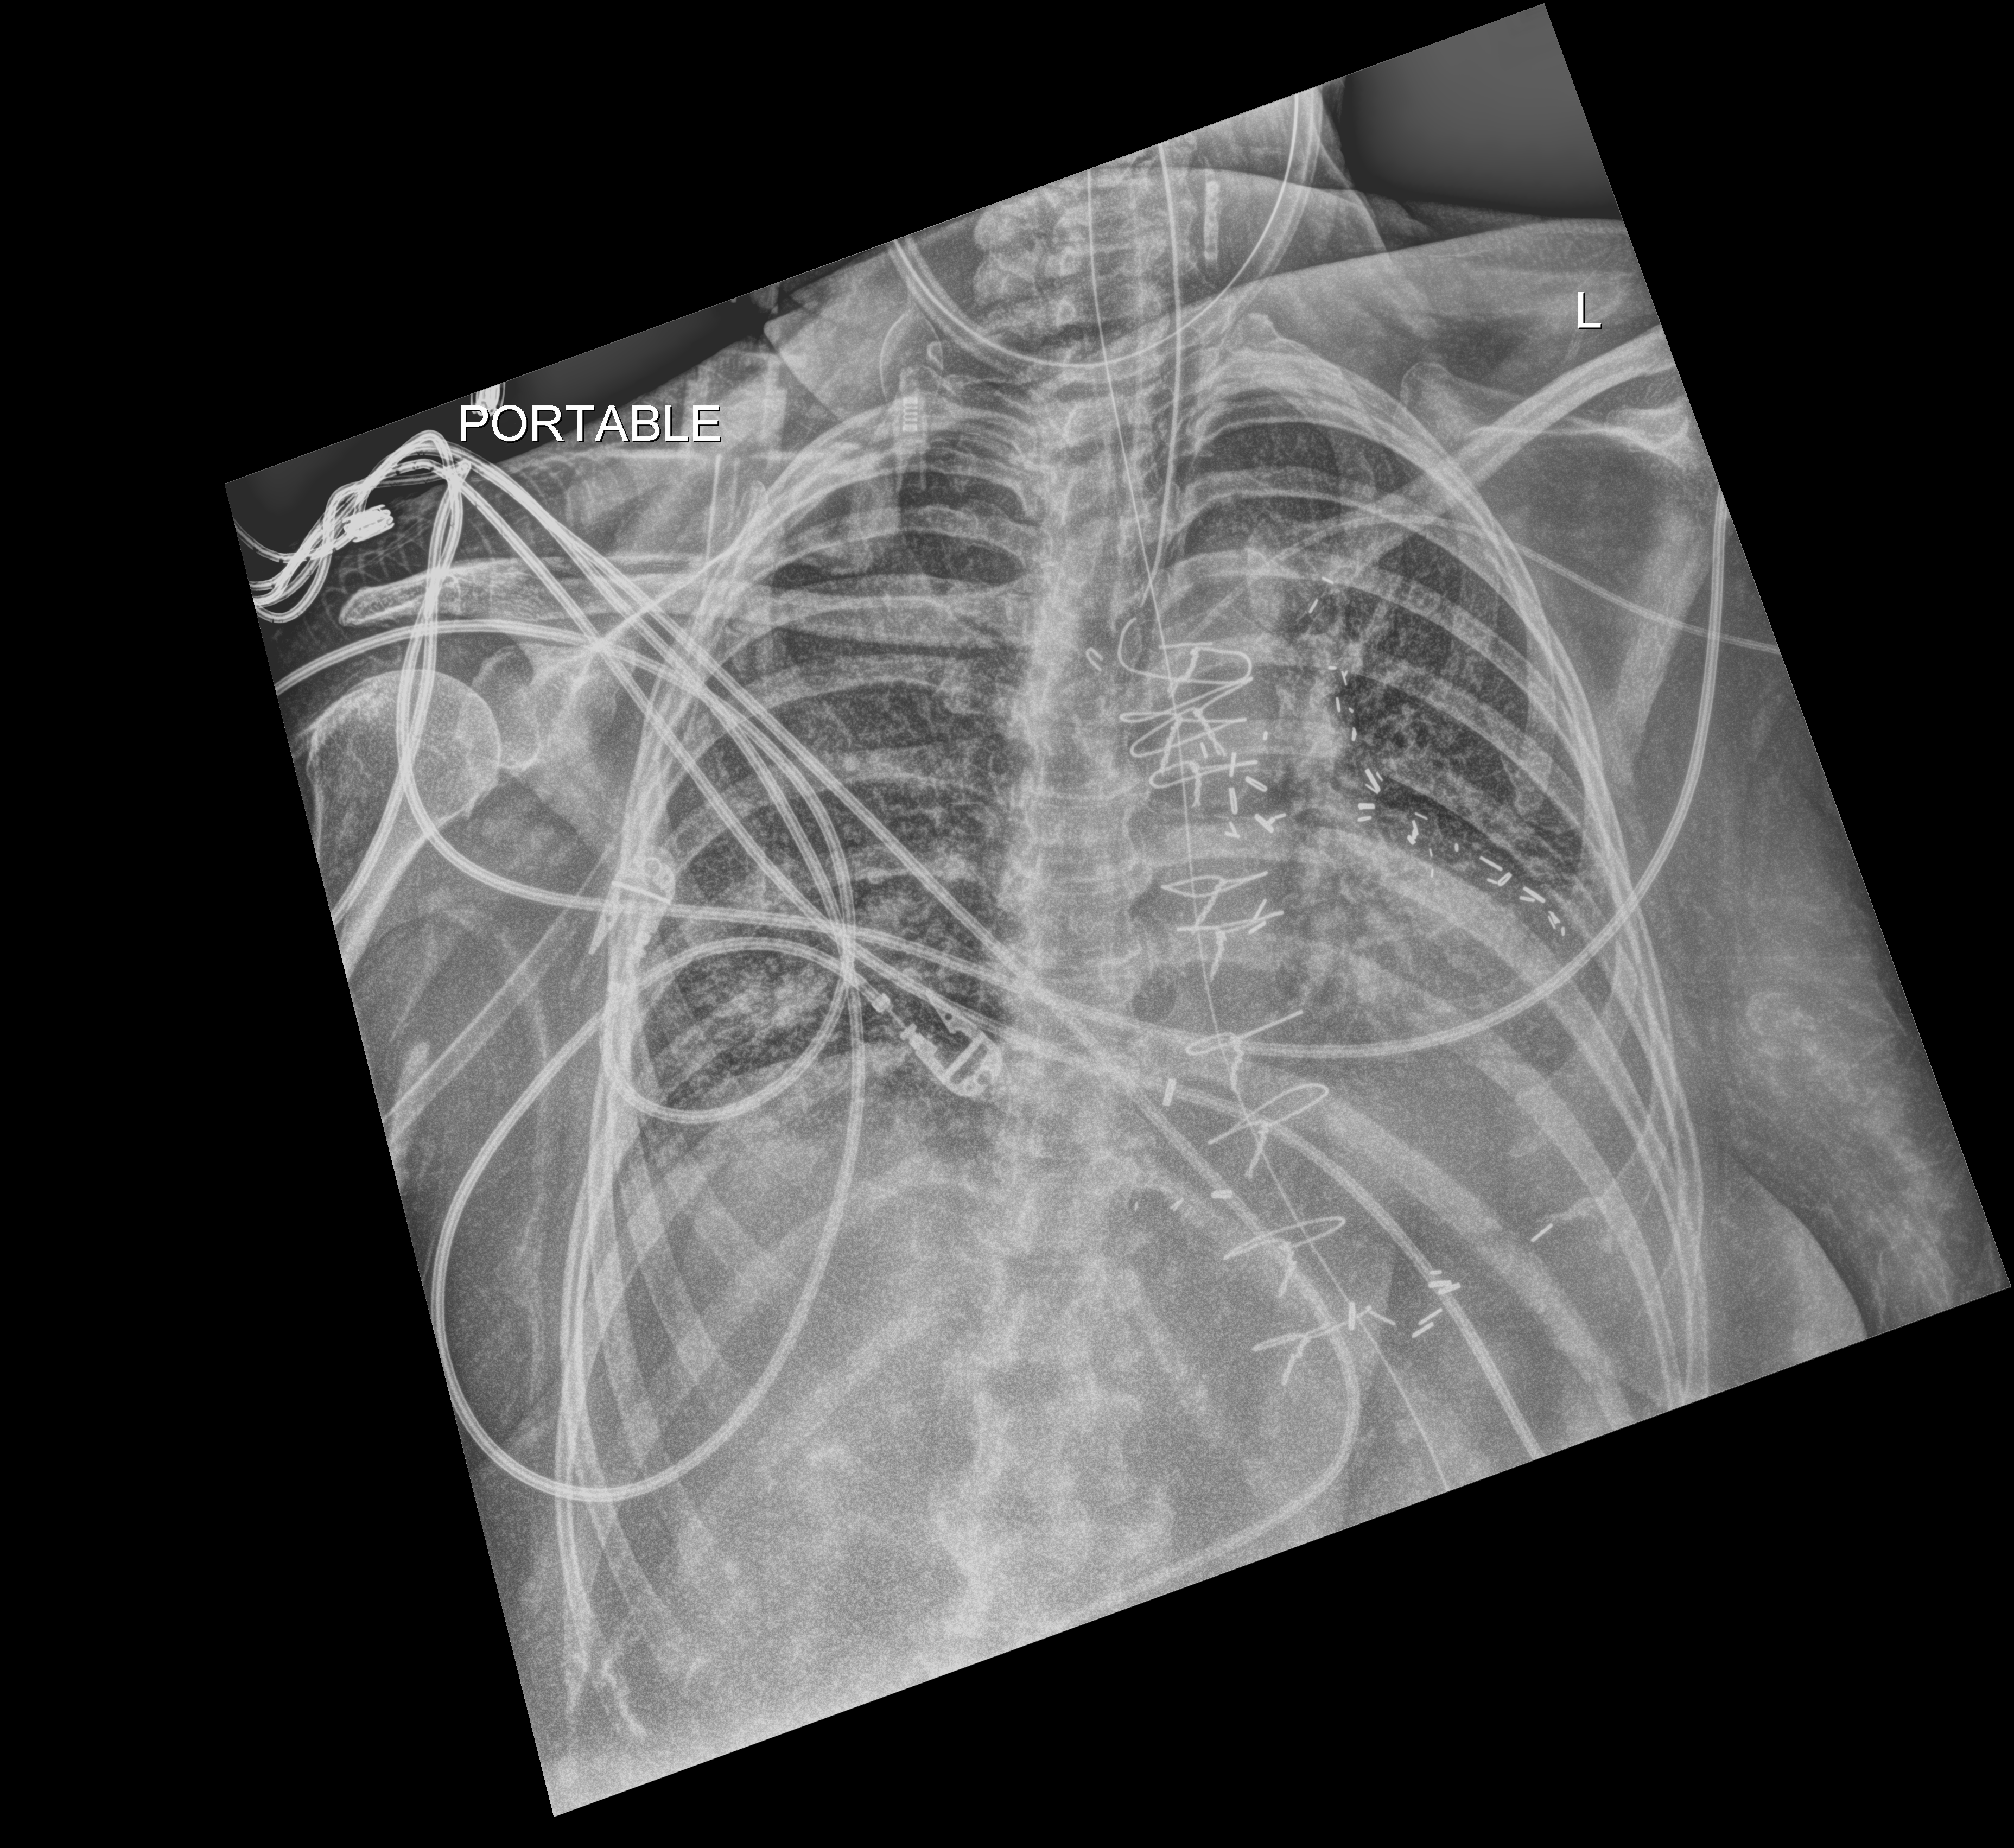
Portable chest radiograph. Patient hospitalised with COVID-19; female, aged 60–74 years.
From the hospital-stay record, not from the radiograph (when in the stay this image was taken is not recorded): COPD (admission record): no; admitted to intensive care during this hospital stay: yes.